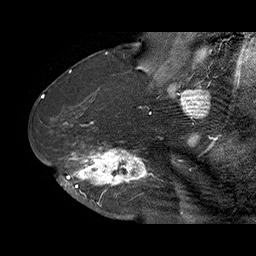
Breast MRI (dynamic contrast-enhanced), one sagittal slice. Dynamic contrast-enhanced series, time point 2 of 6 at this slice position (early post-contrast). 1.5 T. TE 4.5 ms, TR 32.4 ms. 3 mm slice thickness. 256 × 256 image matrix, field of view 180 × 180 mm. Female patient. Case-level facts recorded for this patient, not image findings: setting: breast cancer imaged before/during neoadjuvant chemotherapy; receptor status: HR-positive, HER2-negative.
Structures marked on this image (semi-automatic segmentation, software-assisted and operator-edited):
- analysis volume of interest (the breast-tissue region the enhancement analysis was run in; not a lesion): bounding box (x1, y1, x2, y2) in pixels: (71, 128, 159, 202)
- tumour enhancement mask (voxels above the 100 % enhancement threshold inside the analysis volume of interest): (71, 143, 155, 199)